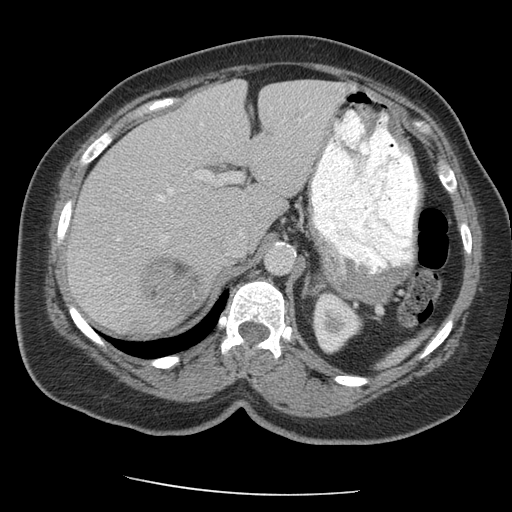
Contrast-enhanced abdominal CT, one axial slice. Slice 130 of 163 in the series (ordered by position). 140 kVp. Intravenous contrast given. Soft-tissue window (W 400 / L 40 HU). 2.5 mm slice thickness. 512 × 512 image matrix. Female patient, age 70 years. From the clinical record (not read from this slice): diagnosis: adrenocortical carcinoma; tumour side: right adrenal; tumour size at pathology: 9.5 cm; Ki-67 index: 5 %; stage (as recorded): 2.
Outlined on this slice (semi-automatic segmentation, software-assisted and operator-edited):
- mass: bounding box [x1, y1, x2, y2] px = [143, 258, 198, 307]